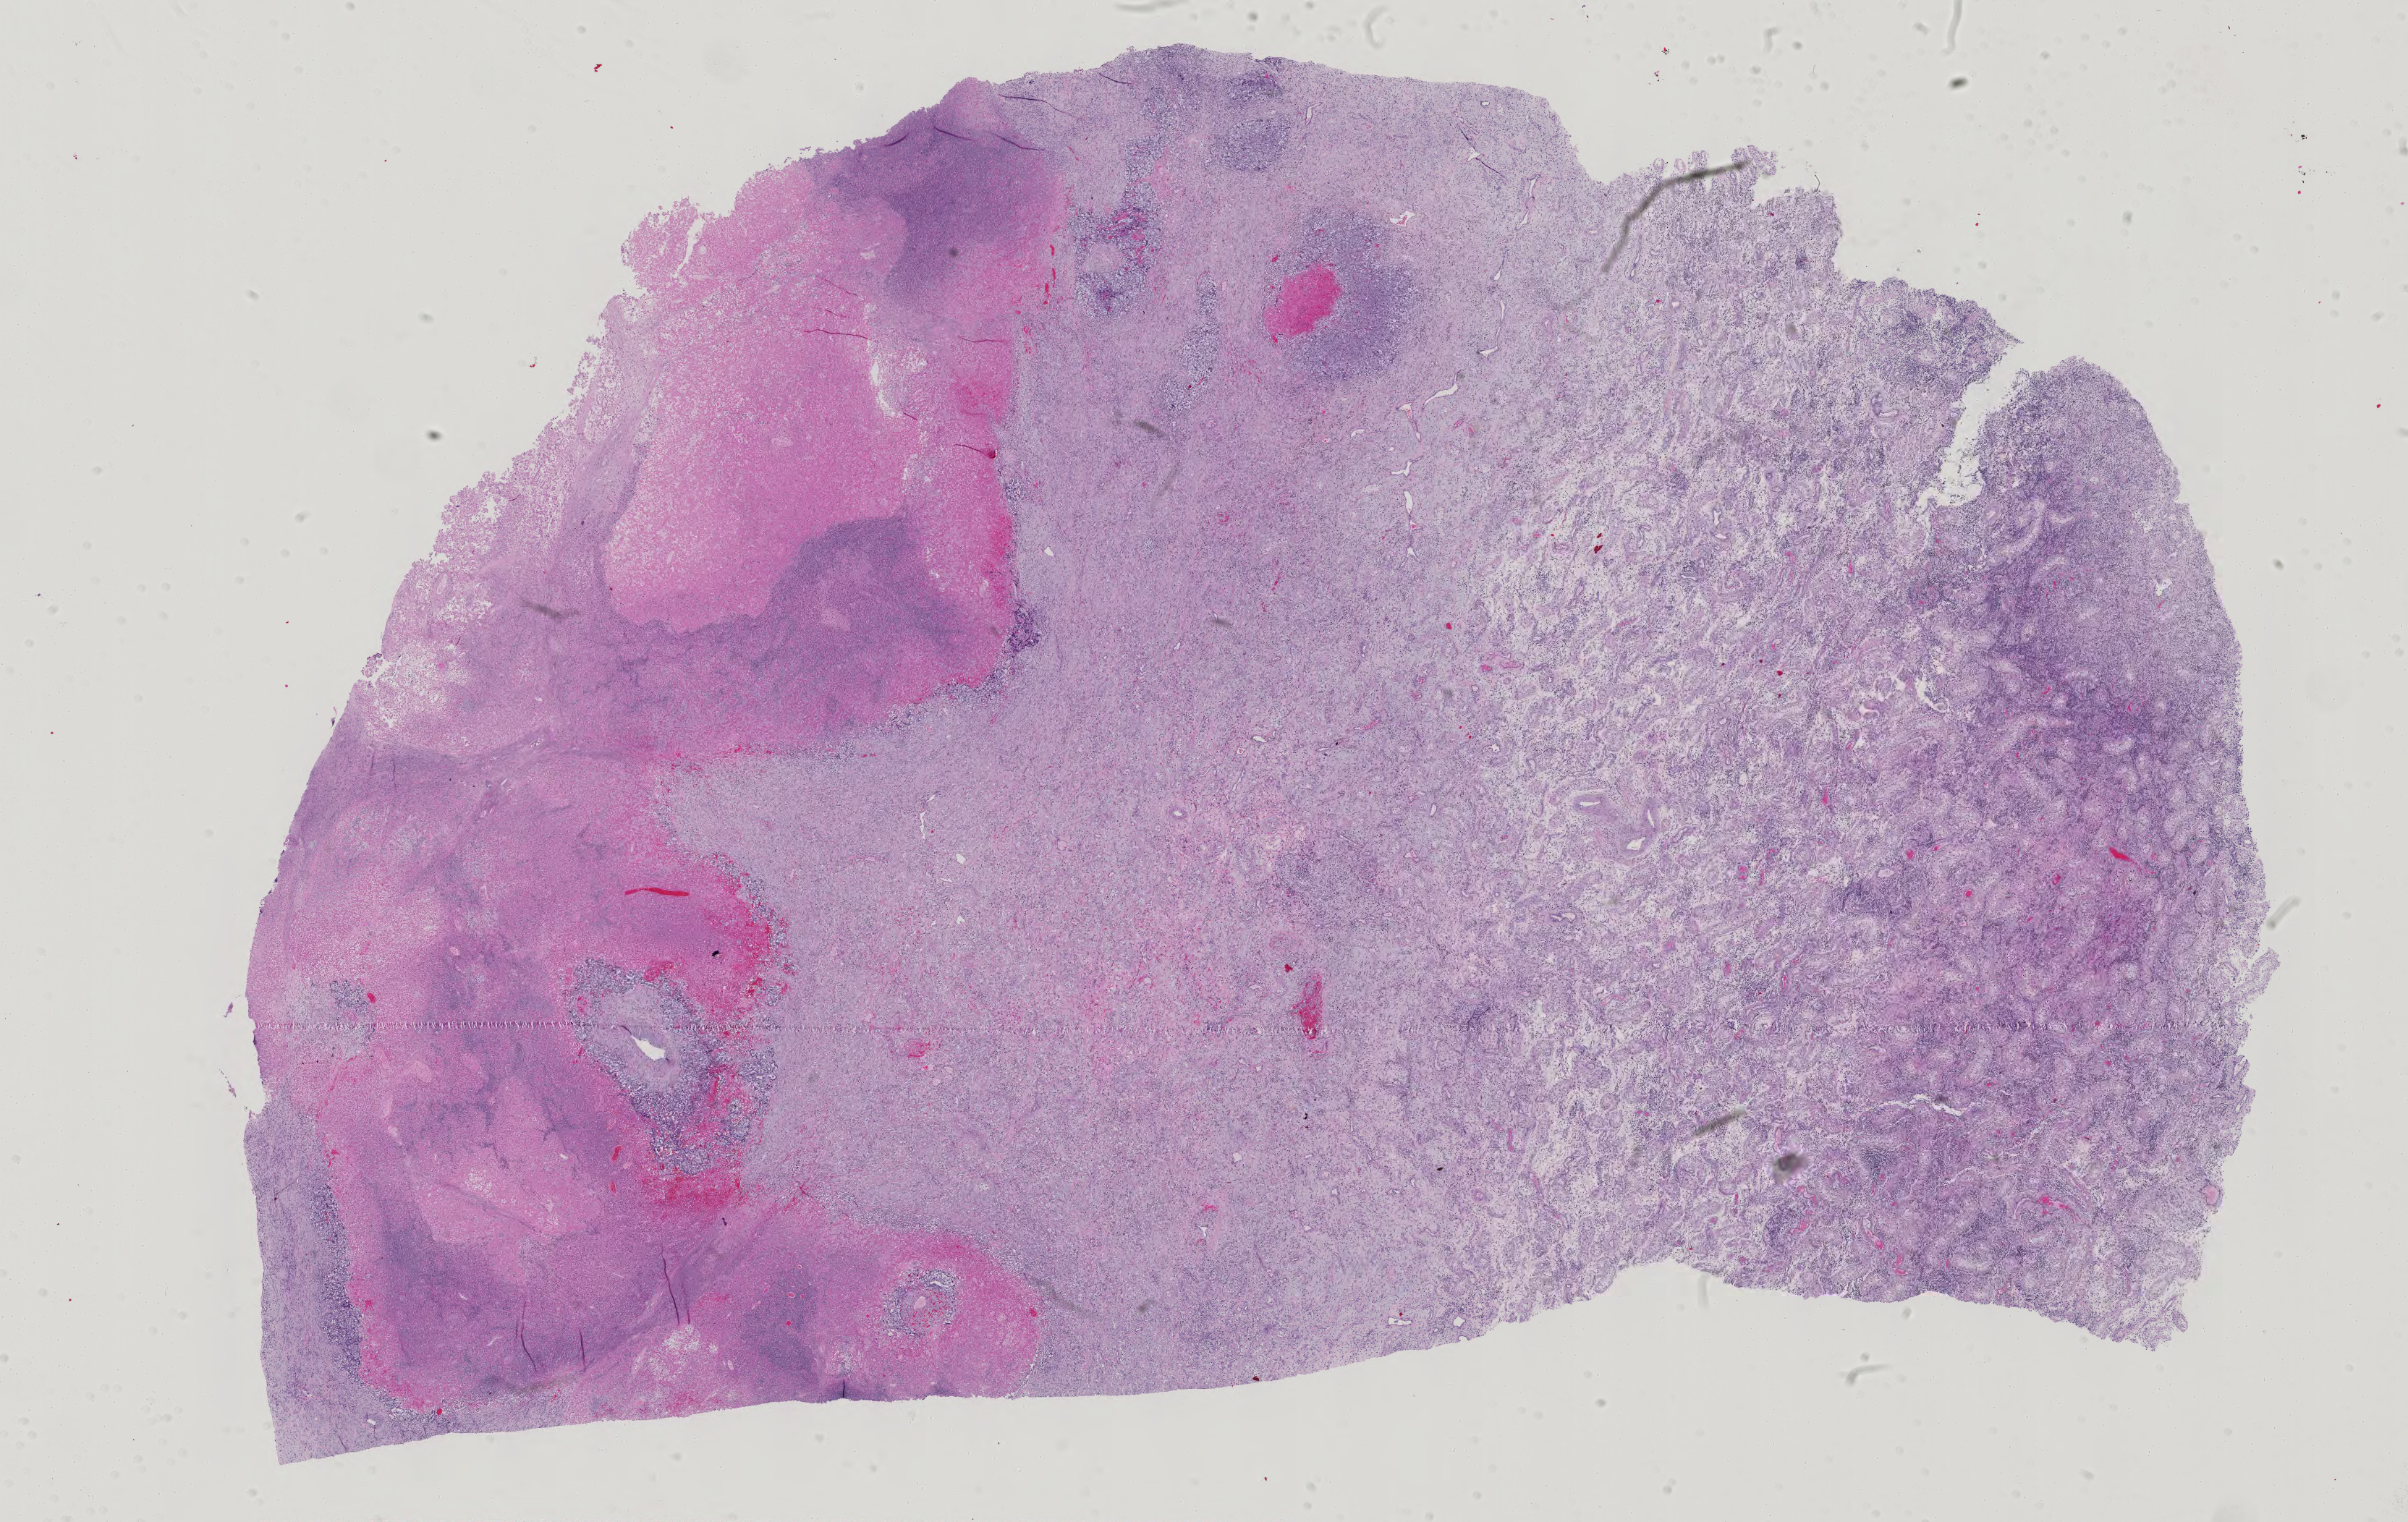
Digitized H&E-stained tissue section (whole slide) — whole scanned area (about 24.2 x 15.3 mm, slide scanned at 40x) shown as a low-resolution overview, formalin-fixed paraffin-embedded (FFPE) diagnostic section, primary tumour sample from the testis. Male, age 31 years at initial diagnosis.
Pathologic diagnosis: Embryonal carcinoma, NOS.